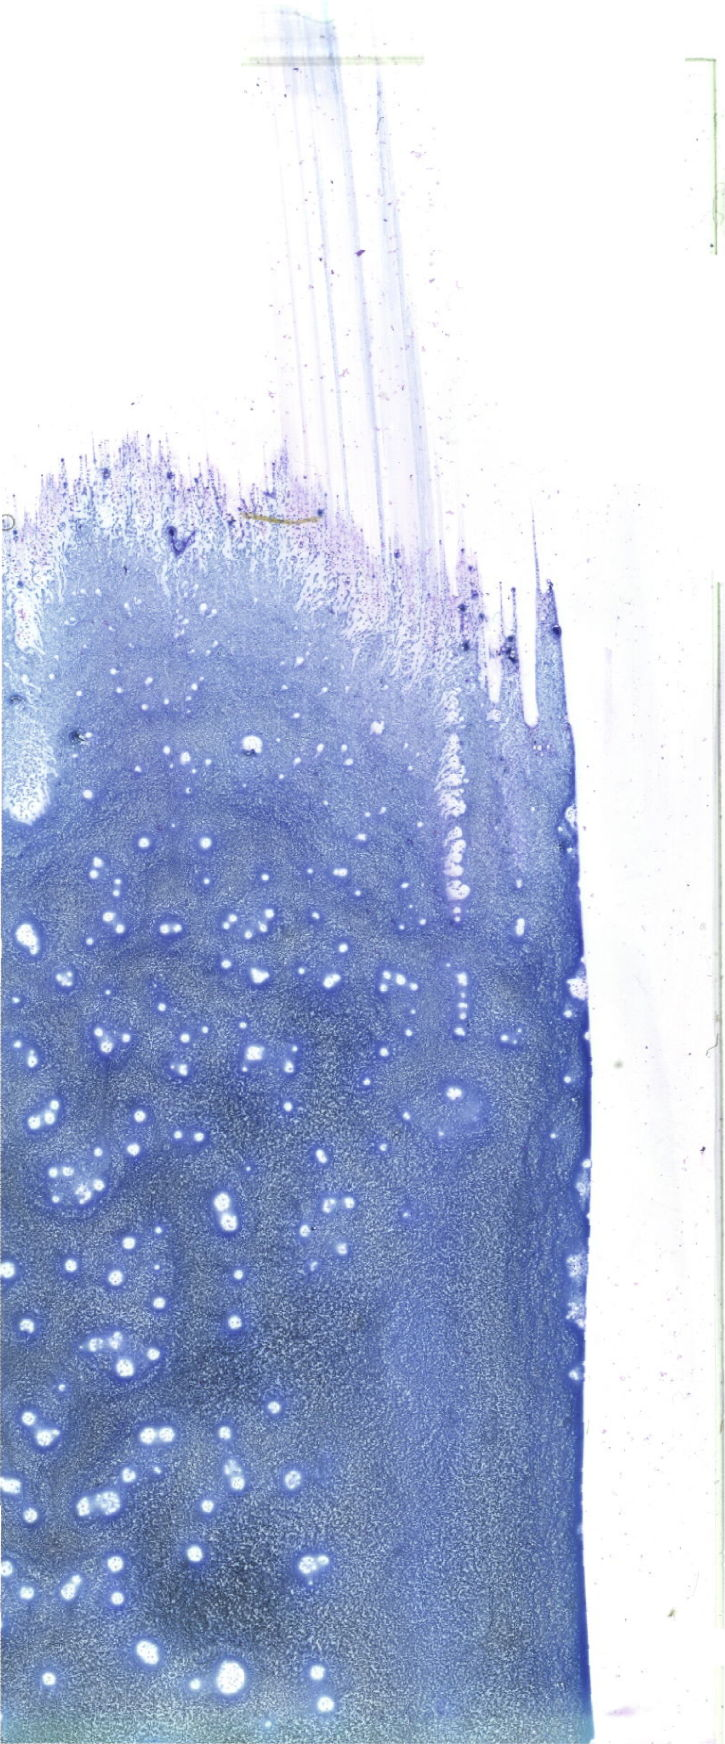
Bone marrow aspirate smear, May-Grünwald-Giemsa (MGG) stain, whole-slide image — low-resolution overview of the scanned area, about 20.6 x 49.4 mm. Male patient.
Diagnosis: Acute Myeloid Leukemia with Maturation.